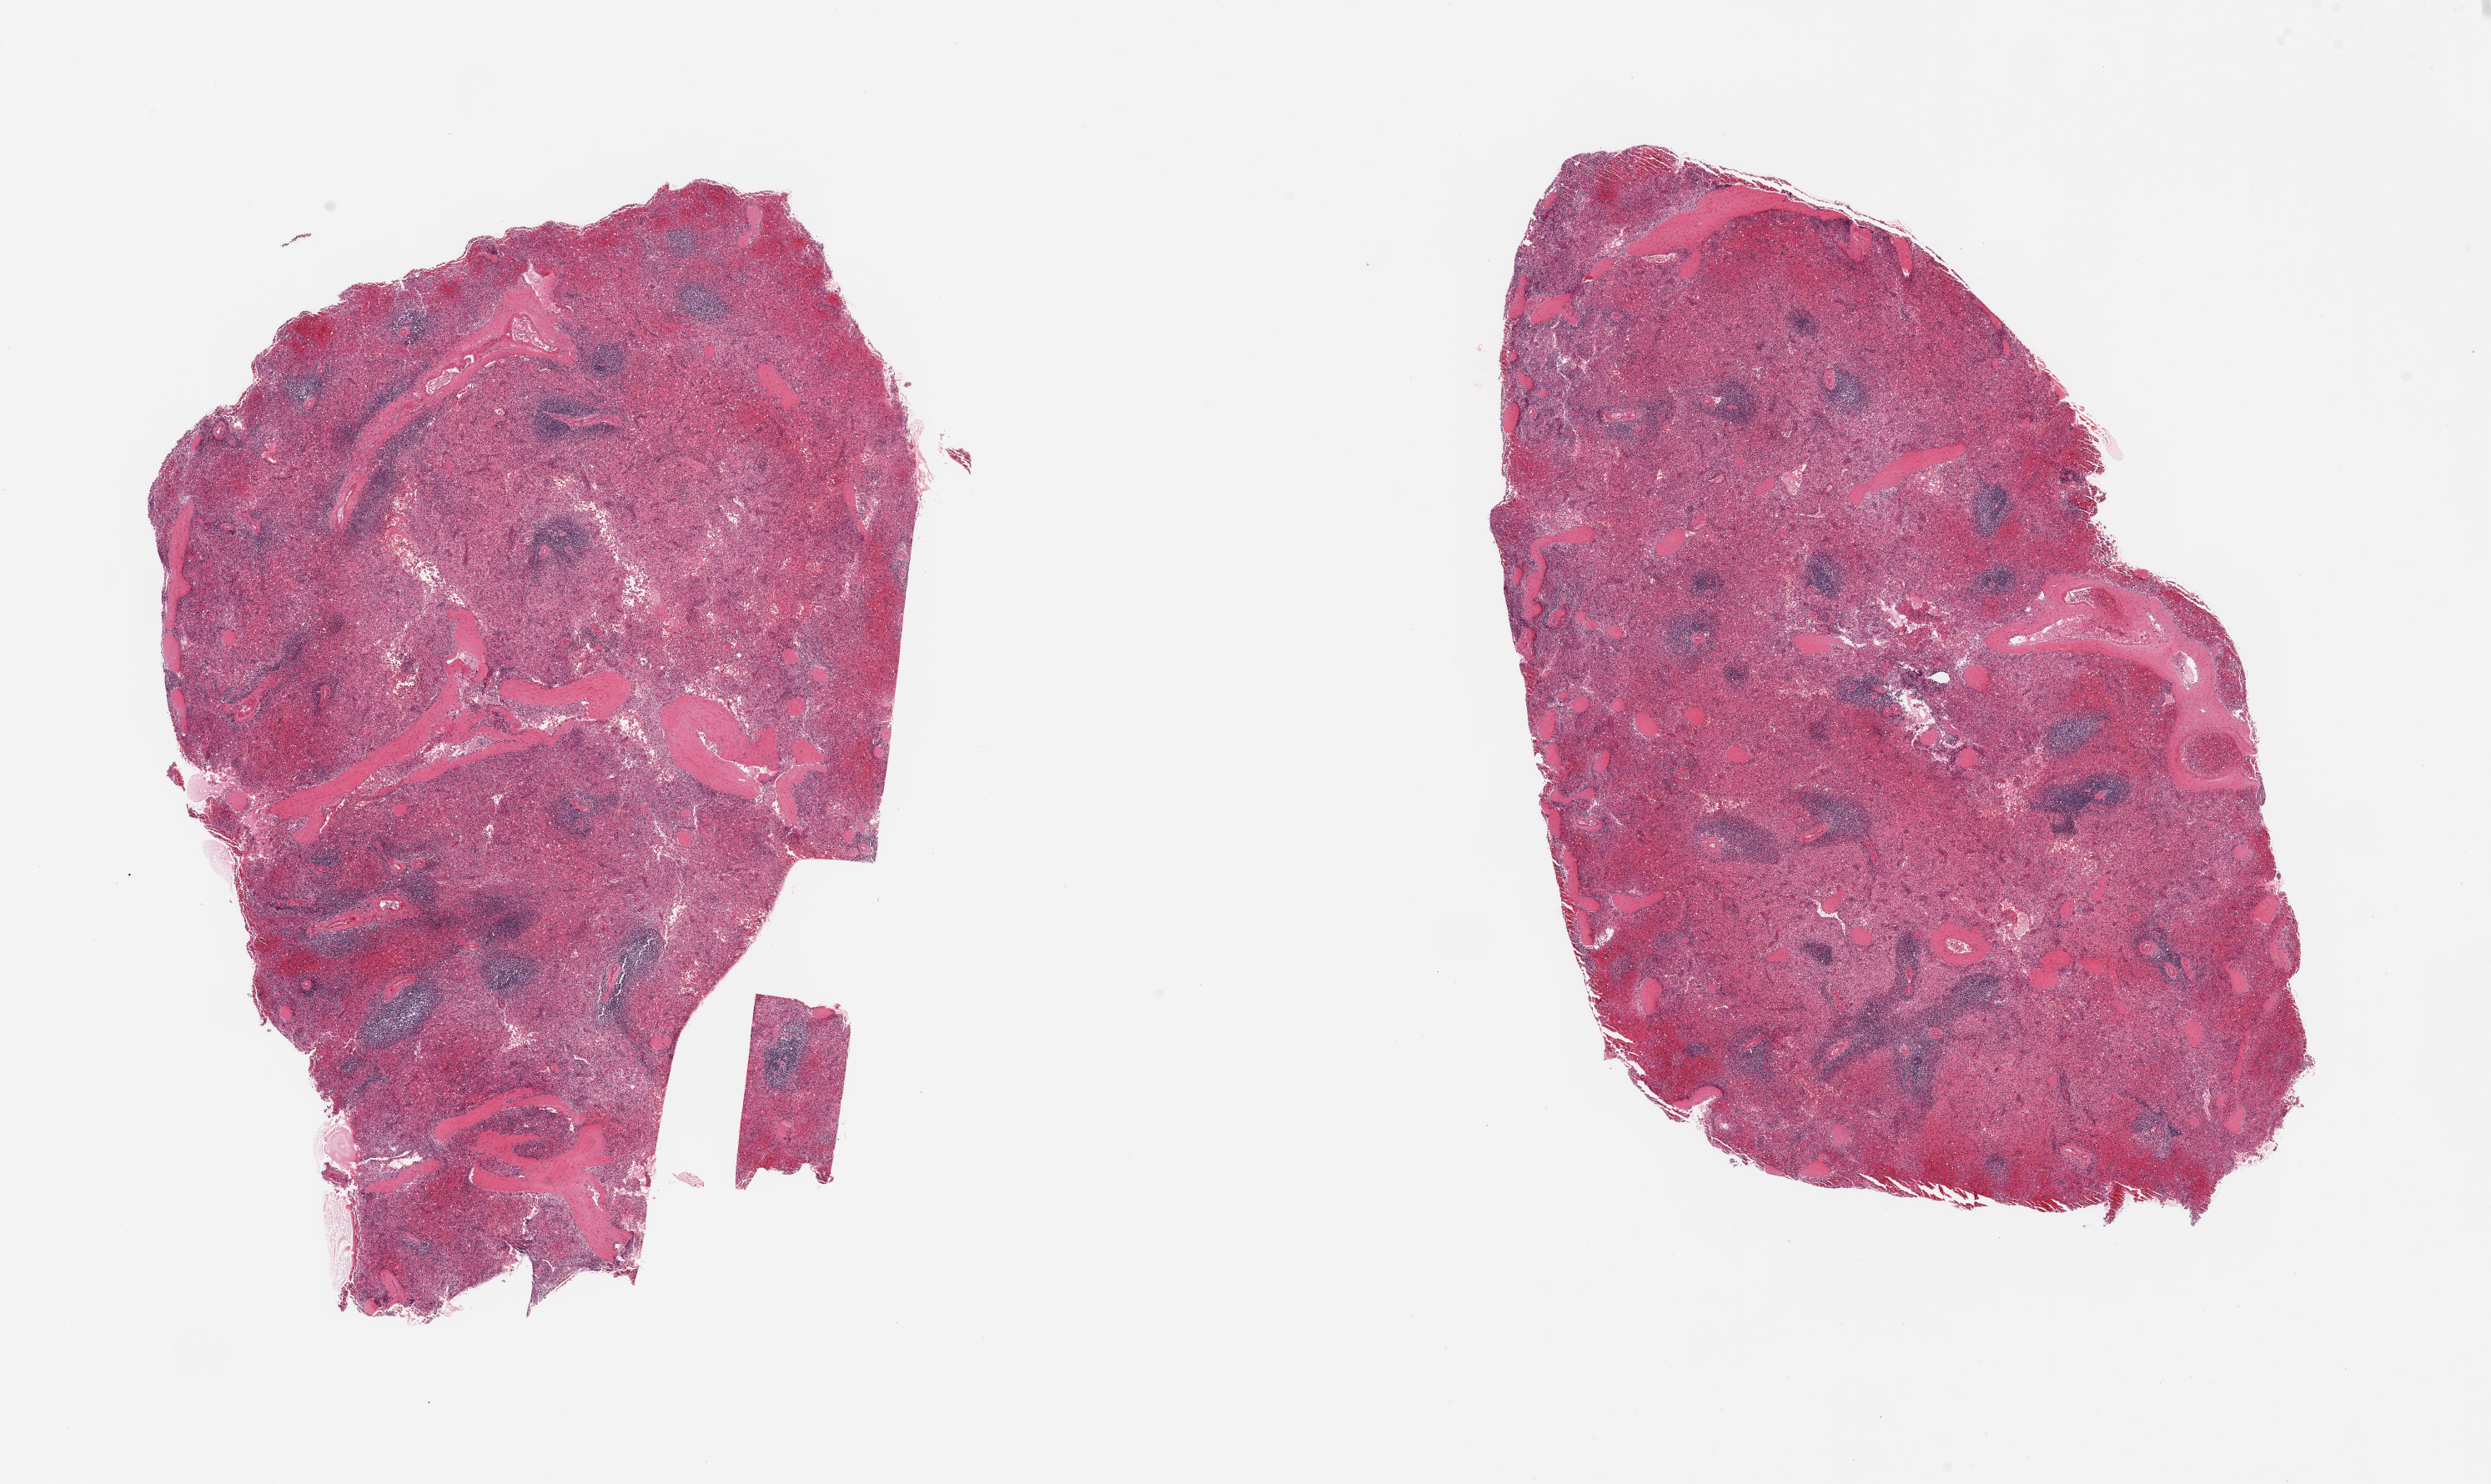
Digitized H&E-stained section — whole scanned area (about 23.6 x 14.1 mm, from a 20x scan) shown as a low-resolution overview; PAXgene-fixed paraffin-embedded (PFPE) section; sampled site (target tissue): spleen; donor tissue sample. Donor sex: female.
Review note (as recorded): 2 pieces; moderate congestion.